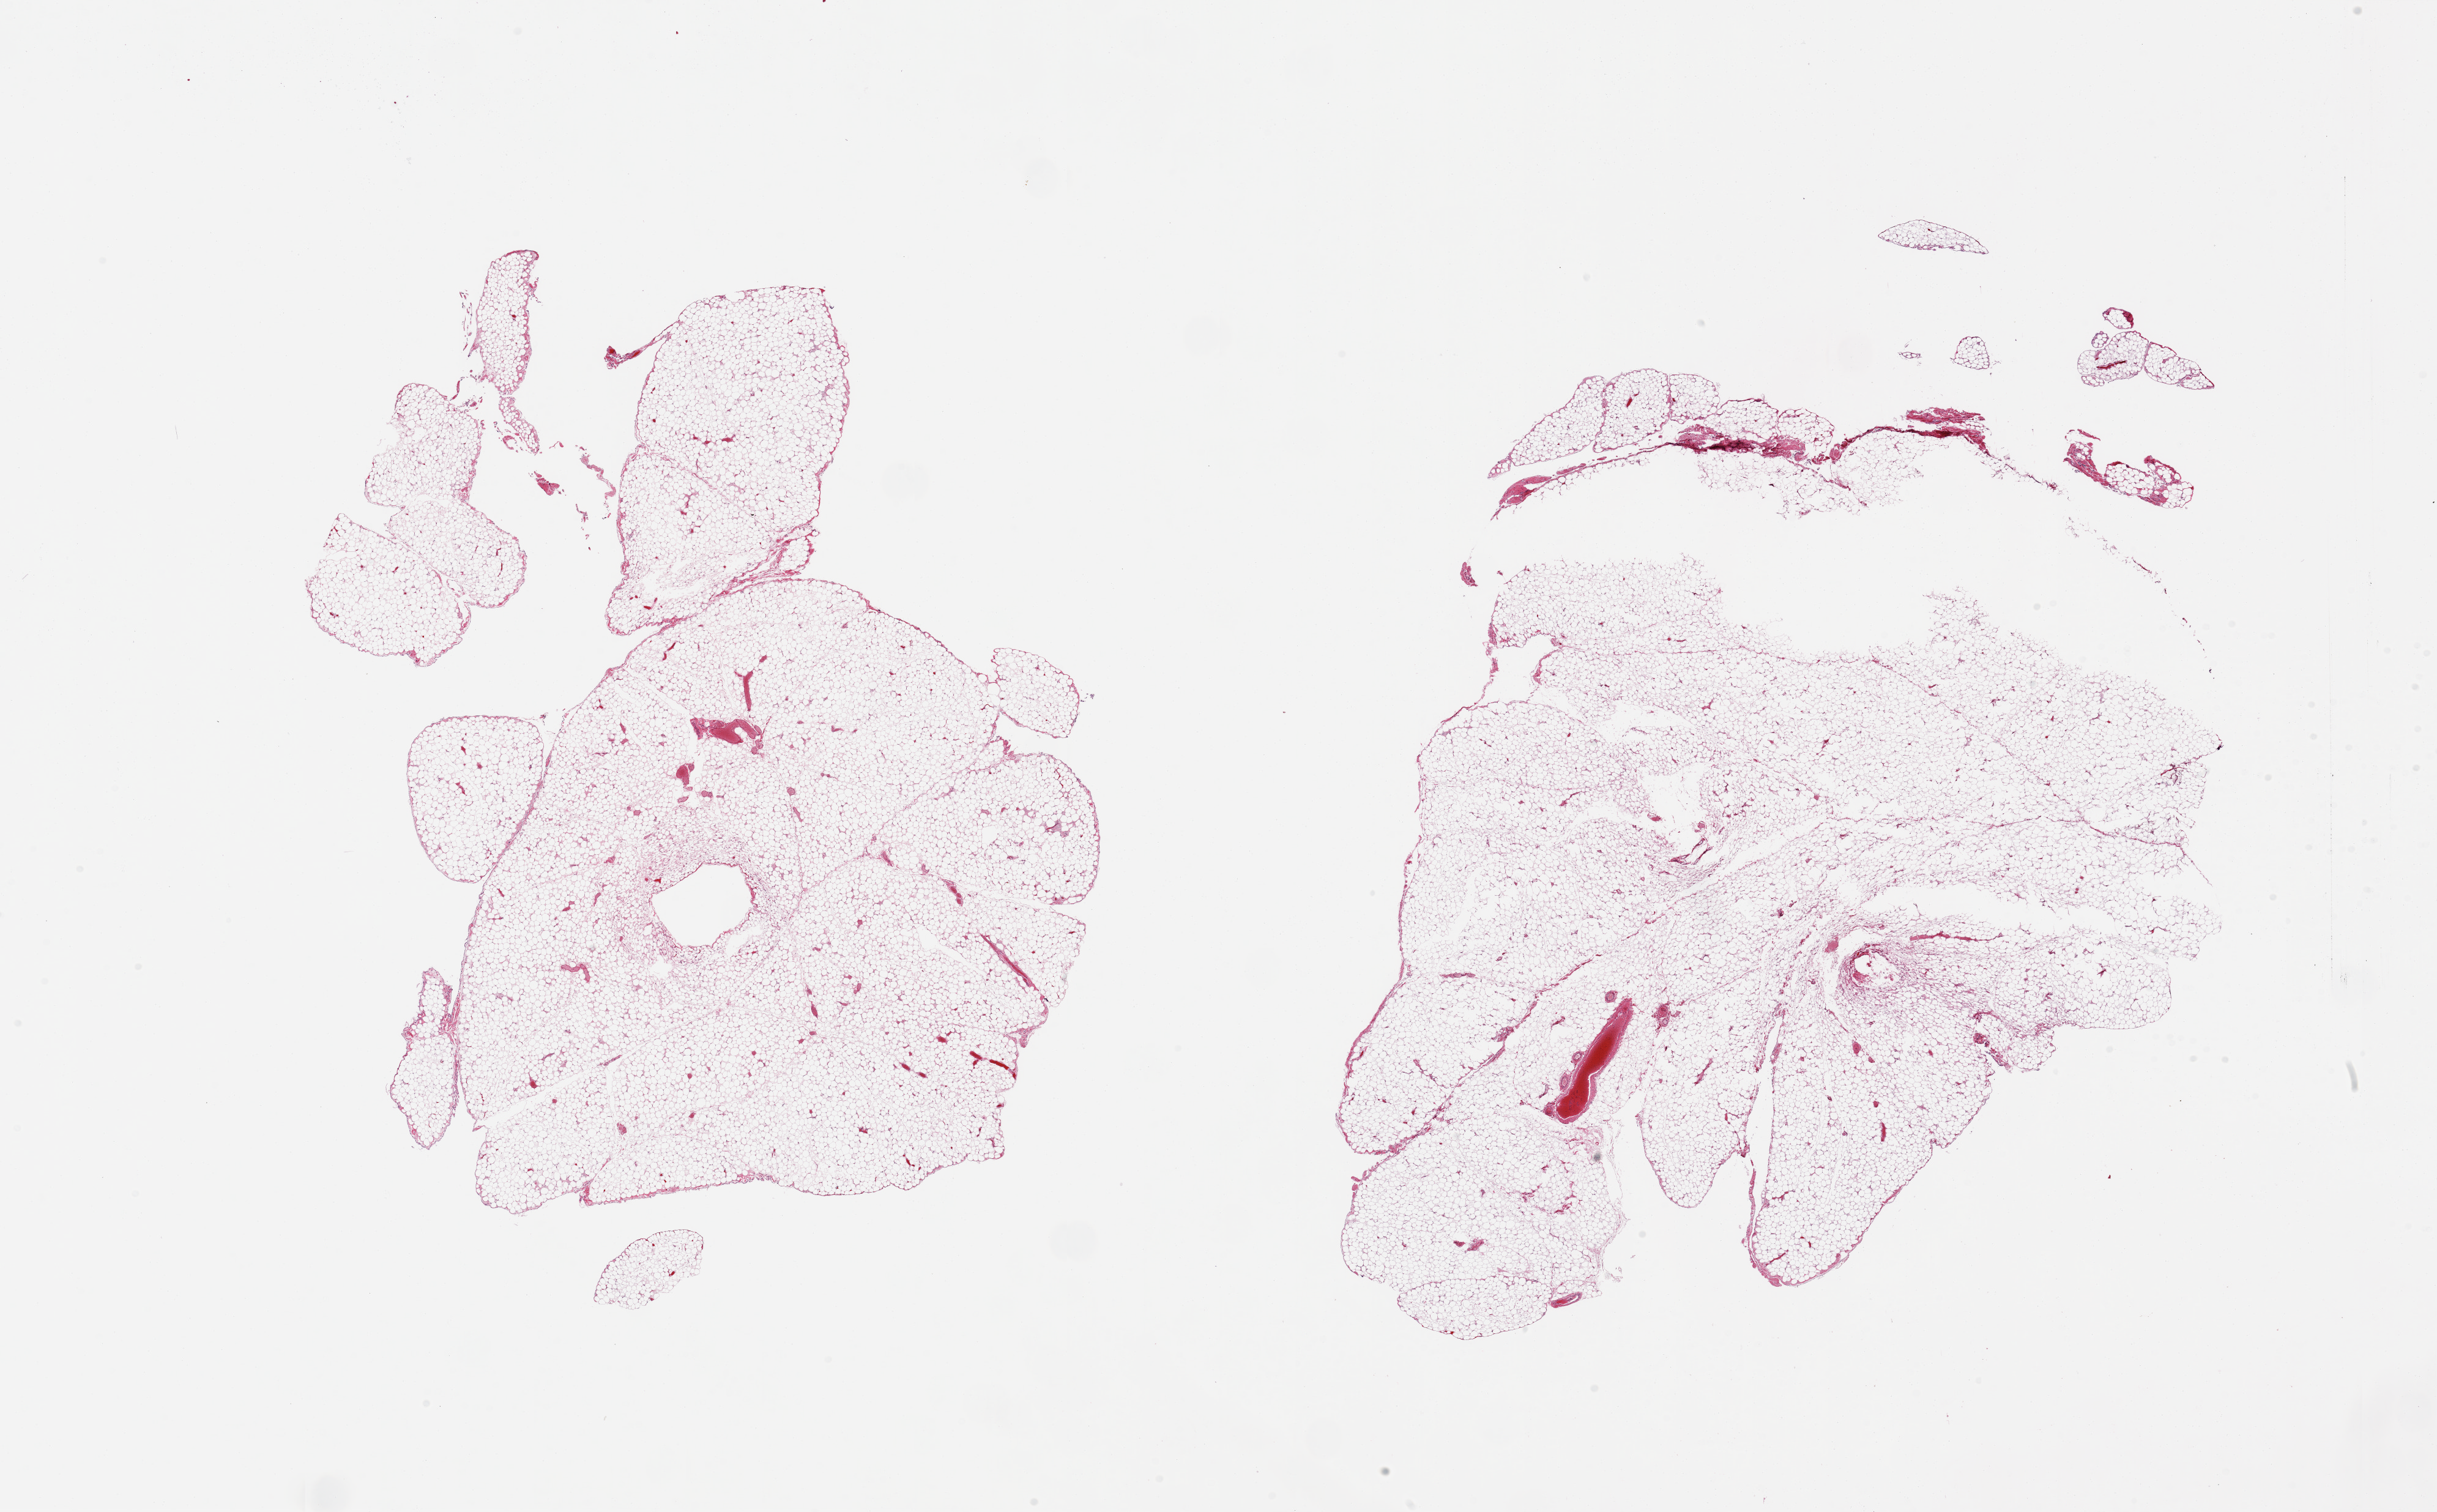
Hematoxylin and eosin (H&E) whole-slide image, brightfield, whole scanned area (about 31.5 x 19.5 mm) shown as a low-resolution overview, PAXgene-fixed, paraffin-embedded tissue, target tissue: omentum, donor tissue sample. Donor: male.
- reviewer comment on this tissue sample: 2 pieces; fibrous content <5%